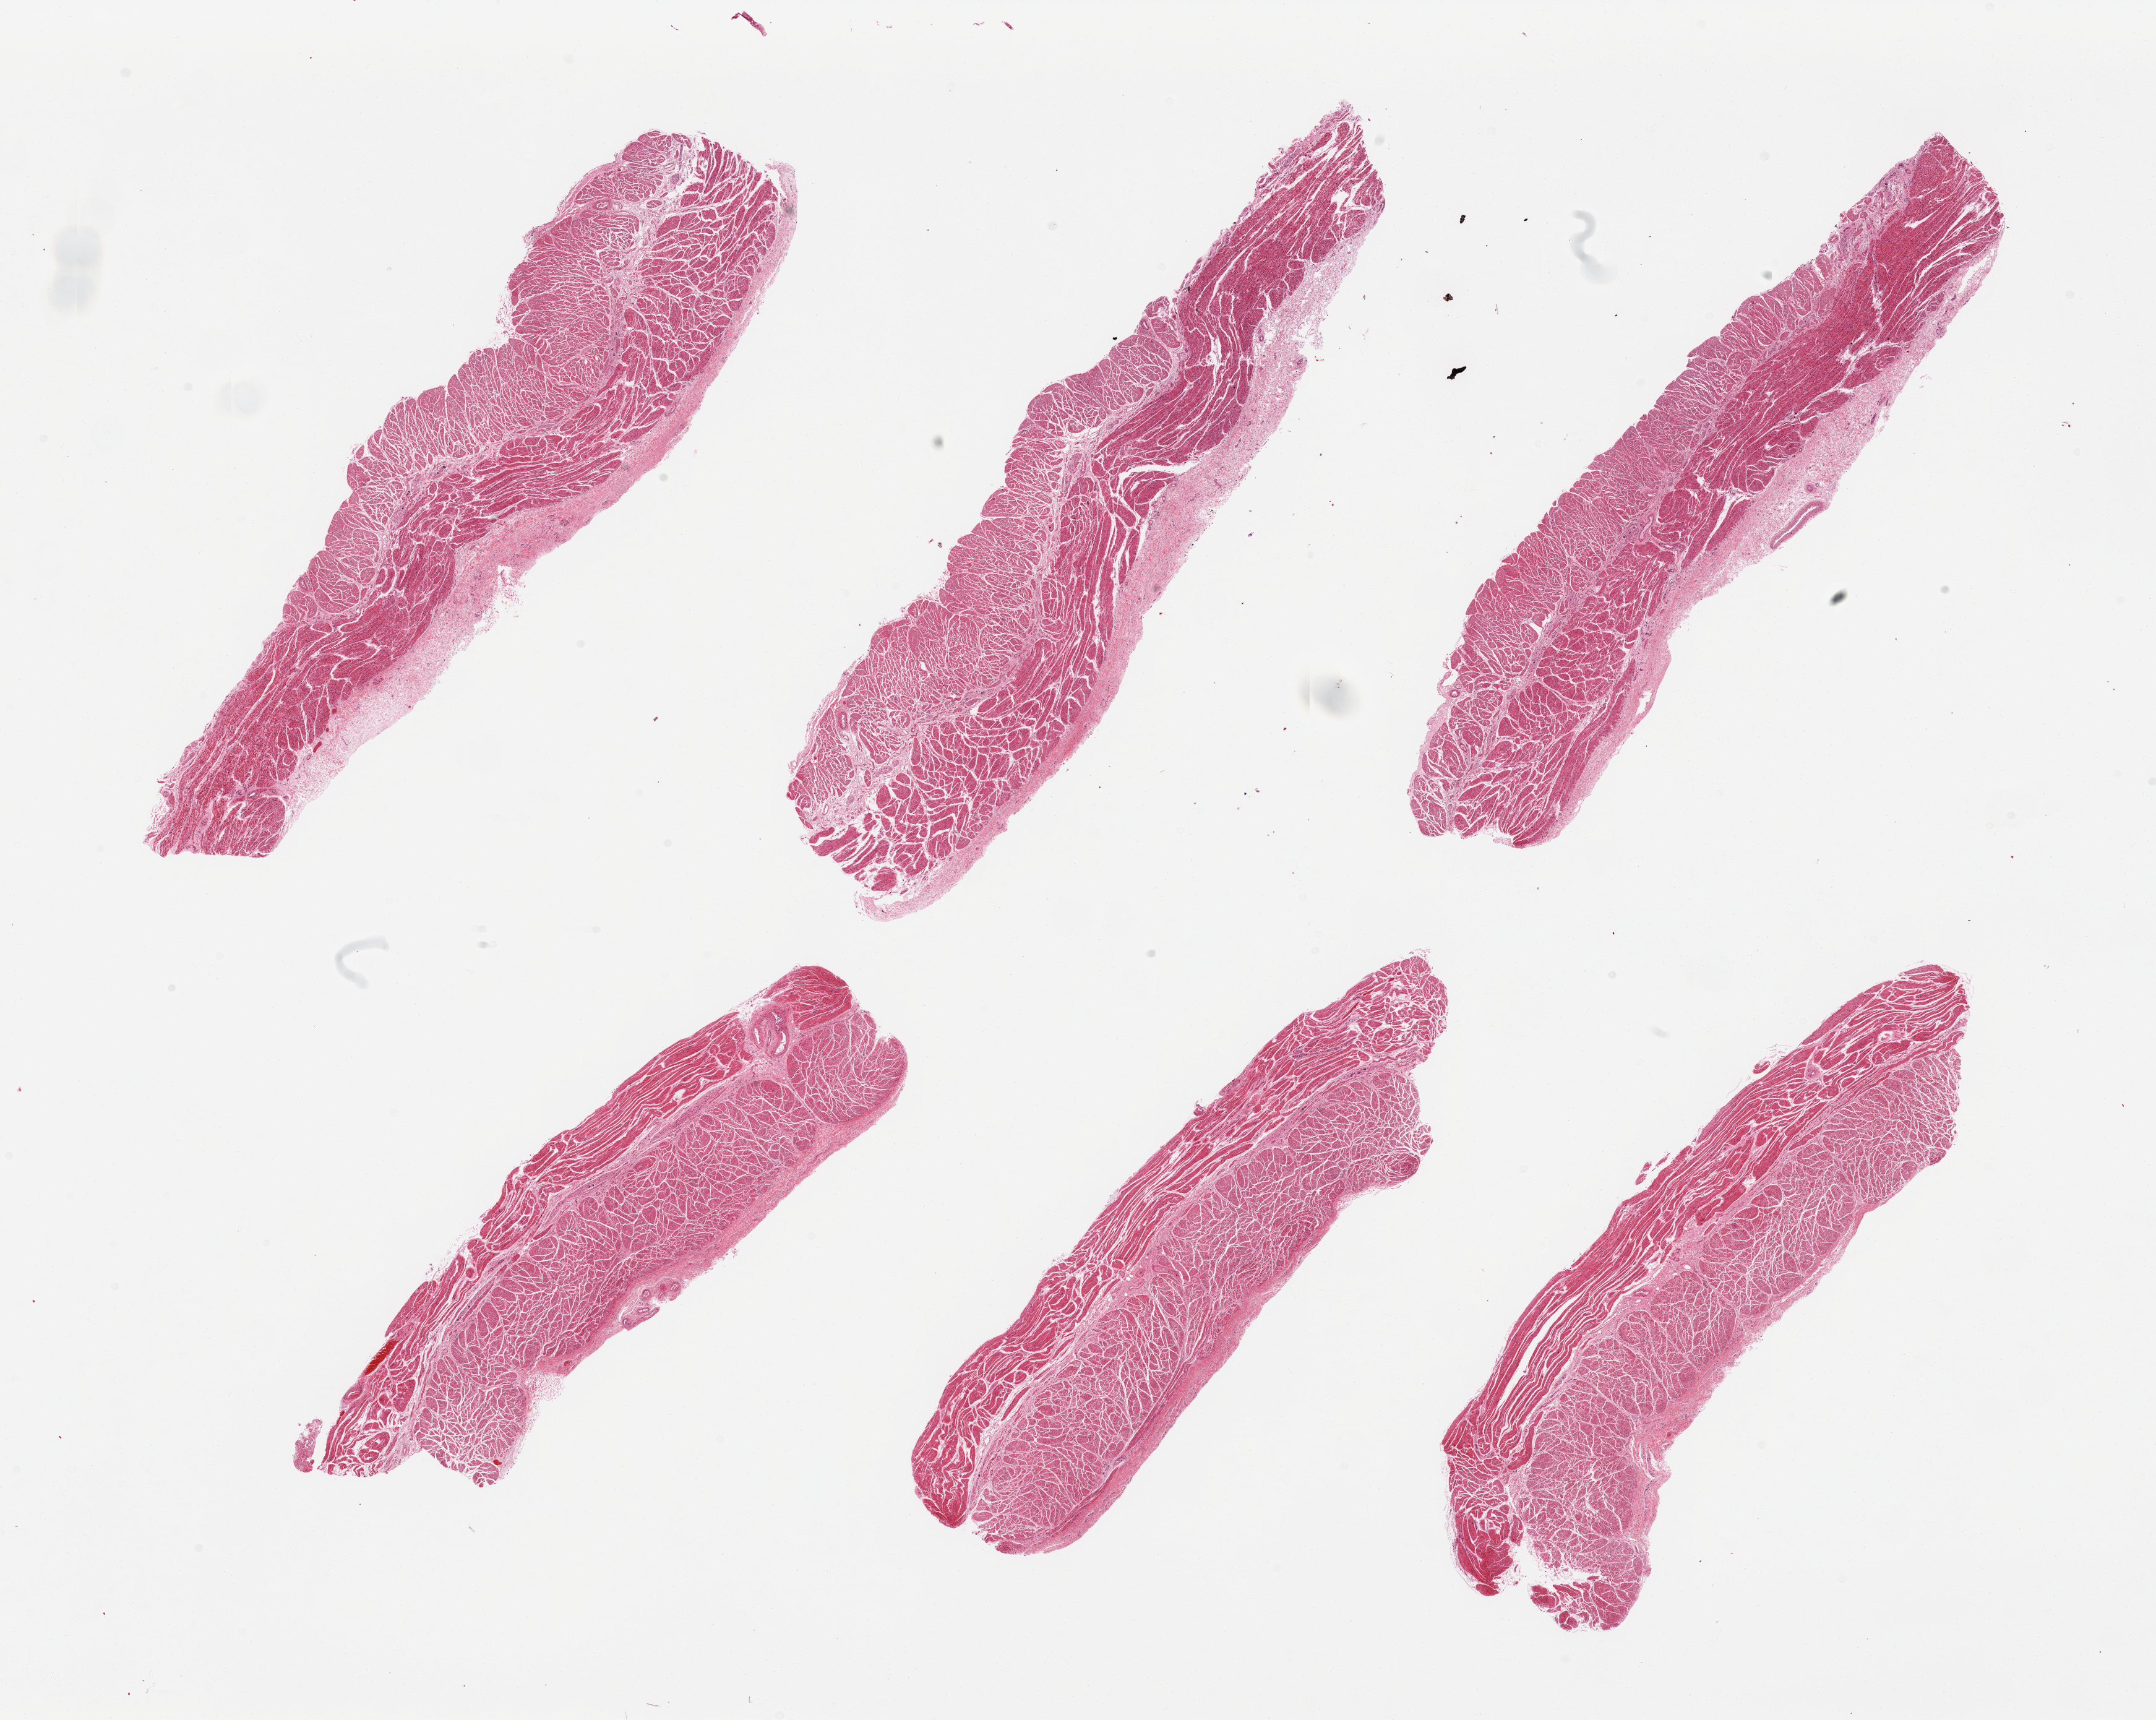
Whole-slide image, hematoxylin and eosin (H&E) stain, a low-resolution overview of the entire scanned area, about 27.6 x 22.0 mm (from a 20x scan); PAXgene-fixed paraffin-embedded (PFPE) section; section of esophageal muscle (target tissue); tissue donor sample. Male donor.
Pathologist's review note for this sample: 6 pieces, well trimmed.